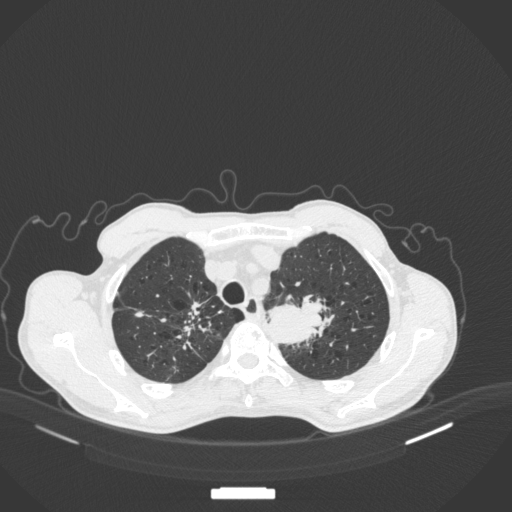
Chest CT, one axial slice. Position 353 of 394 along the scan axis. Reconstruction kernel B31f. 120 kVp. Lung window (W 1500 / L -600 HU). 1 mm slice thickness. 512 × 512 image matrix, field of view 400 × 400 mm. Patient: male, 65 years. Case-level facts recorded for this patient, not image findings: clinical TNM (as recorded): T2b N0 M0.
Annotated regions visible in this slice (bounding box drawn by a radiologist):
- lung tumour (recorded histology: adenocarcinoma): bounding box <268,286,340,350> (left, top, right, bottom; pixels)